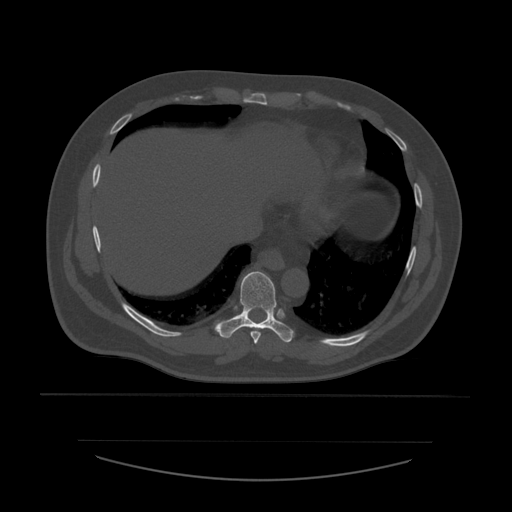
CT including the spine, one axial slice; slice 321 of 532 in the series (ordered by position); bone window (W 1800 / L 400 HU); 1.25 mm slice thickness; 512 × 512 image matrix, field of view 441 × 441 mm. Patient age 44 years. Case-level facts recorded for this patient, not image findings: primary cancer: soft tissue sarcoma.
Outlined on this slice (semi-automatic segmentation, software-assisted and operator-edited):
- T8 vertebra: bounding box <251,332,261,344> (left, top, right, bottom; pixels)
- T9 vertebra: <215,272,294,343>